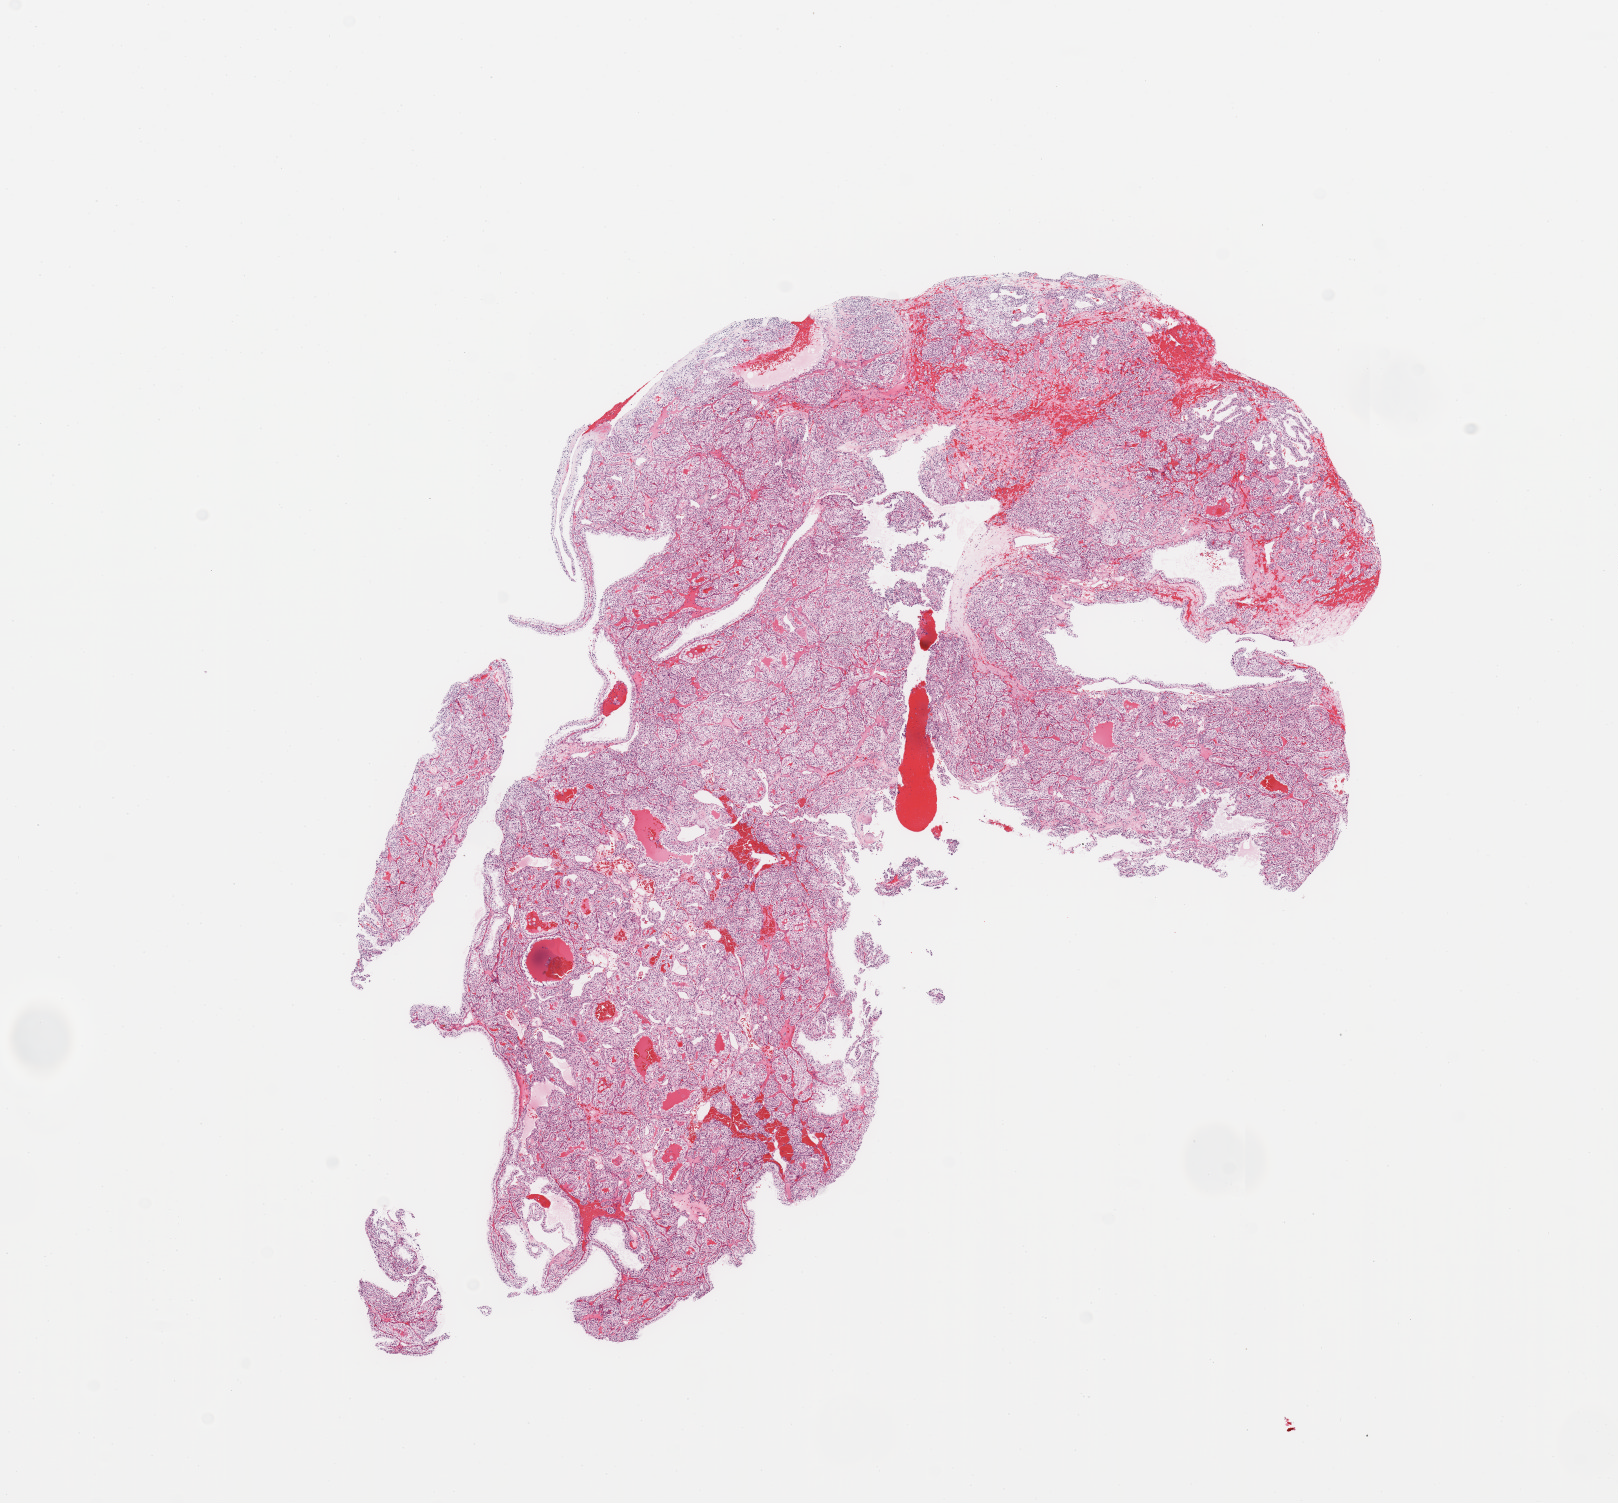
Whole-slide histology image, H&E — whole scanned area (about 12.8 x 11.9 mm) shown as a low-resolution overview; tumour tissue sample, sampled site: kidney. Male, 35 y/o.
Histologic diagnosis: Renal cell carcinoma, NOS.